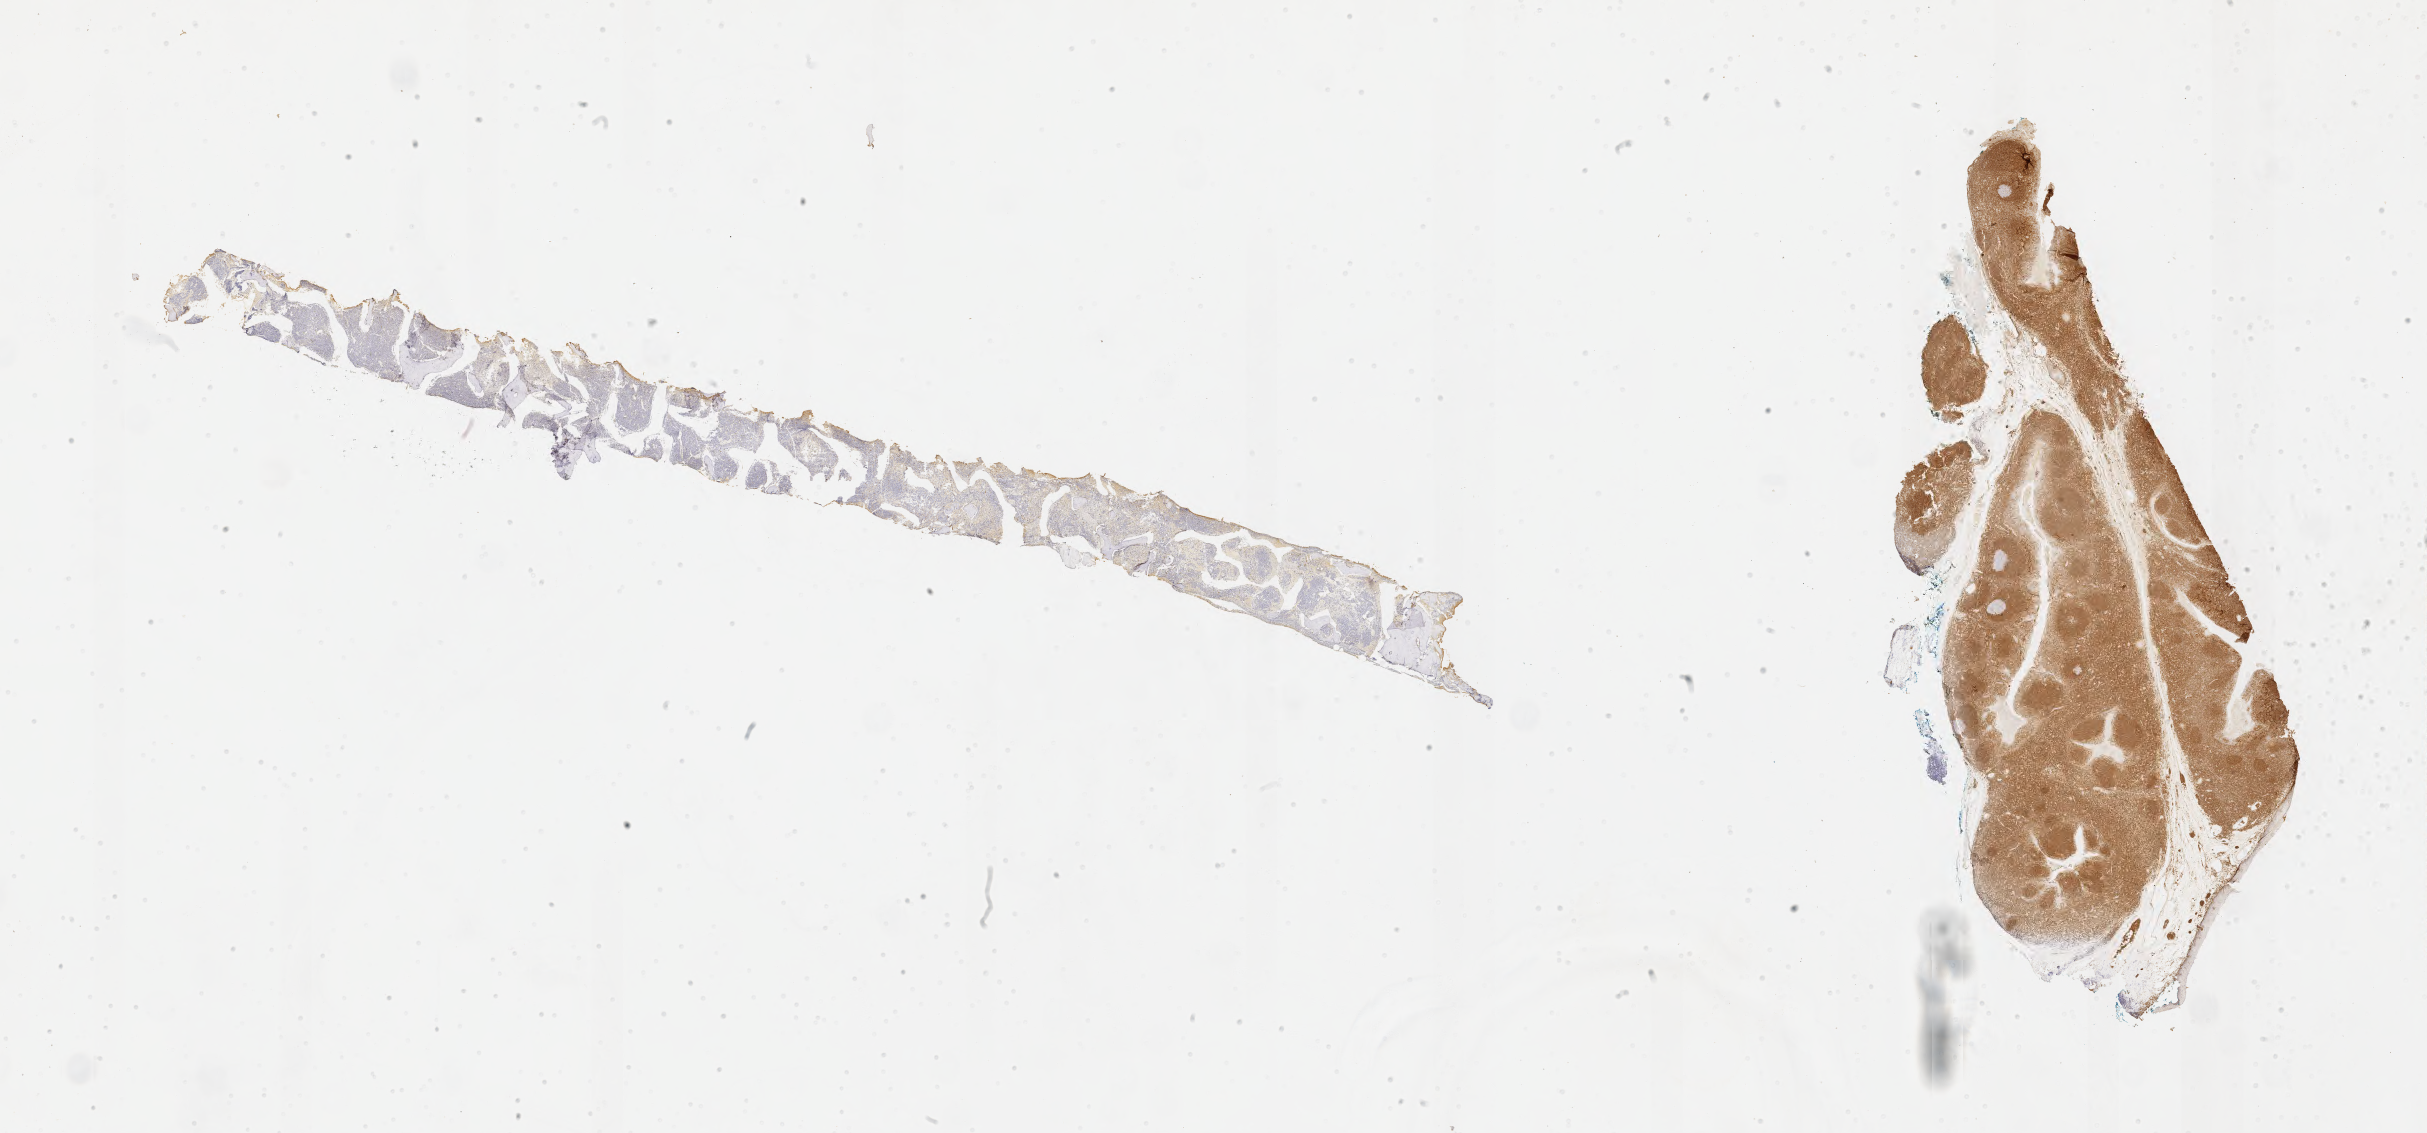
IHC for BCL2, whole-slide image, shown as a low-resolution overview of the whole scanned area (about 39.2 x 18.3 mm), tumor tissue, site: bone marrow. Male patient, aged 18.
Diagnosis: Burkitt lymphoma, NOS.